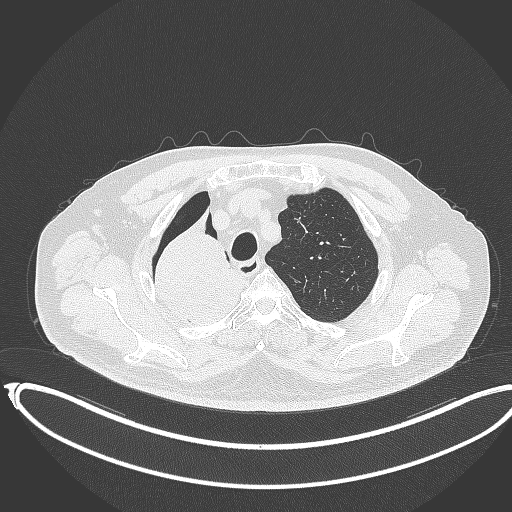
Chest CT, one axial slice; position 302 of 403 along the scan axis; reconstruction kernel B70f; 120 kVp; lung window (W 1500 / L -600 HU); 1 mm slice thickness; 512 × 512 image matrix, field of view 436 × 436 mm. Patient: male, 68 years. From the clinical record (not read from this slice): clinical TNM (as recorded): T2a N0 M0.
Structures marked on this image (rectangle marked by the reading radiologist):
- lung tumour (recorded histology: adenocarcinoma): bounding box [x1, y1, x2, y2] px = [144, 209, 249, 337]